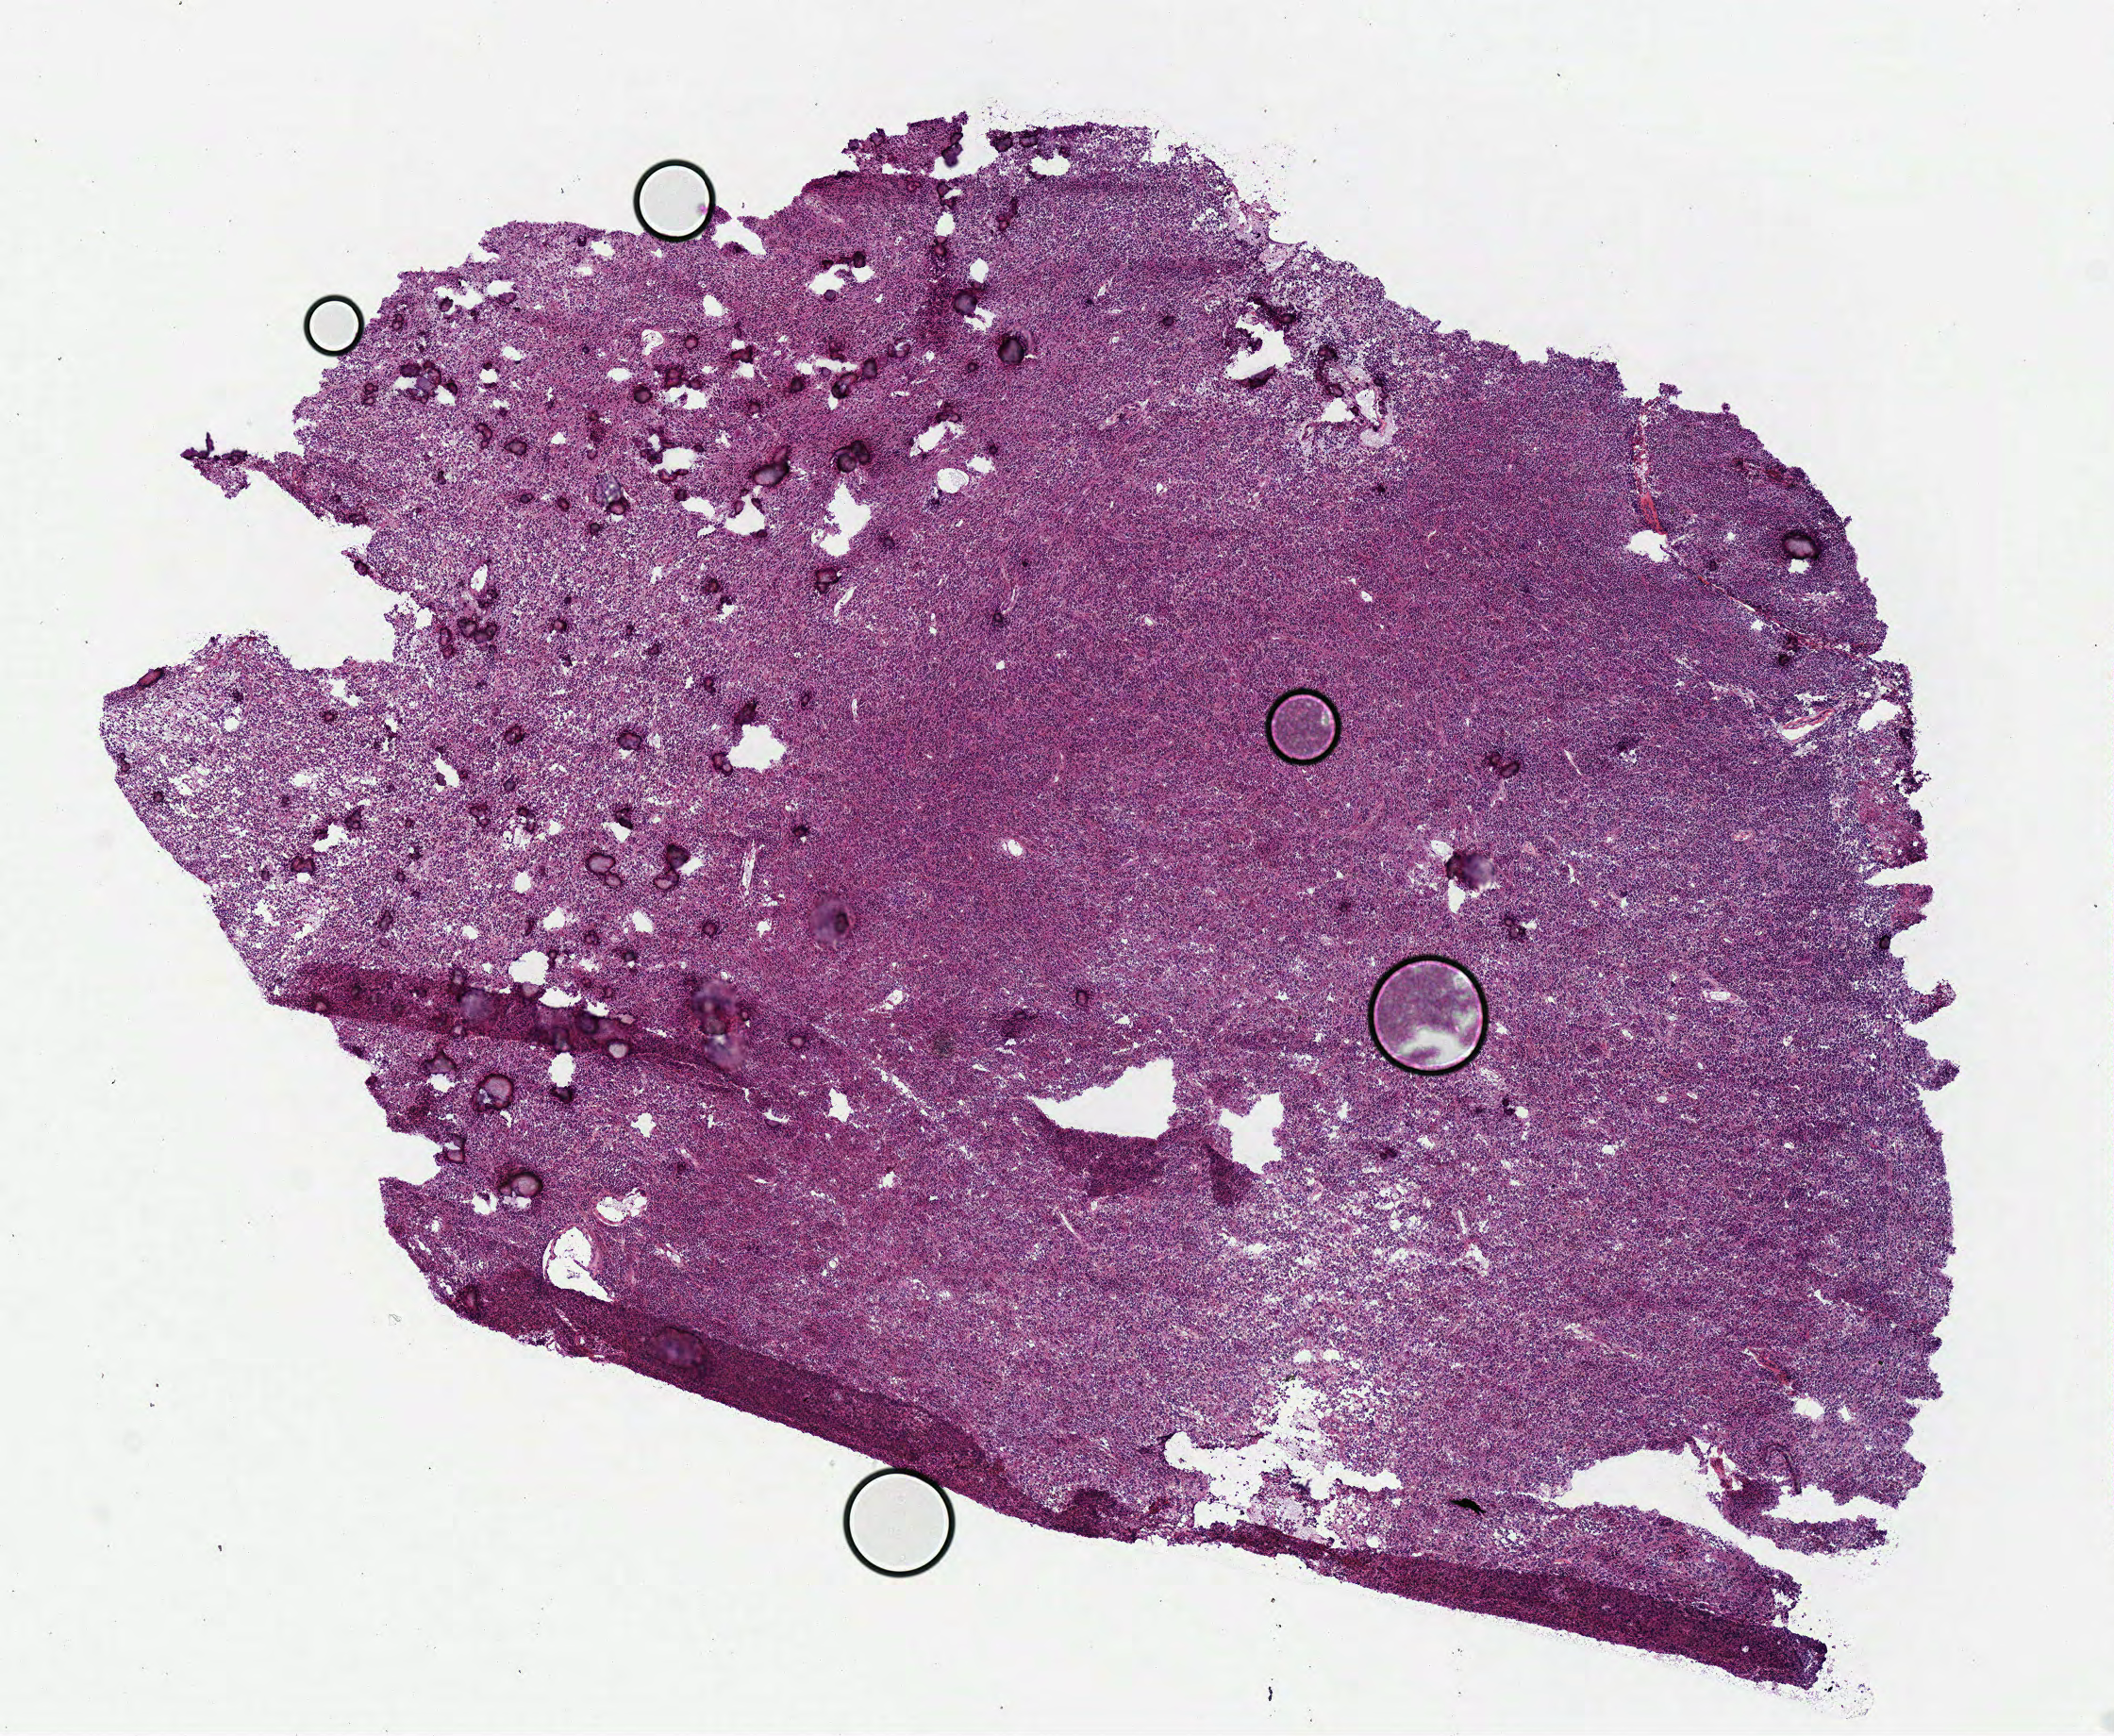
Digitized Hematoxylin and eosin (H&E) stained tissue section (whole slide), a low-resolution overview of the entire scanned area, about 8.8 x 7.2 mm, frozen section from the bottom of the tissue portion, sample: primary tumour, brain. Patient: male, age at initial diagnosis 53 years. Histologic grade: G3 (poorly differentiated). Composition of this section per pathologist review: tumour cells 100%, tumour nuclei 85%, normal cells 0%, stromal cells 0%, necrosis 0%.
- diagnosis: Oligodendroglioma, anaplastic (cerebrum)